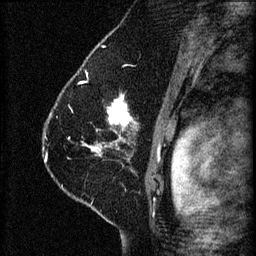
Breast MRI (dynamic contrast-enhanced), one sagittal slice. 3 images stored at this slice position (order not interpretable as contrast timing). 1.5 T. TE 4.2 ms, TR 8.2 ms. 2 mm slice thickness. 256 × 256 image matrix, field of view 180 × 180 mm. Patient: female, 41 years.
Structures marked on this image (semi-automatic segmentation, software-assisted and operator-edited):
- analysis volume of interest (the breast-tissue region the enhancement analysis was run in; not a lesion): bounding box (x1, y1, x2, y2) in pixels: (67, 92, 165, 173)
- tumour enhancement mask (voxels above the 70 % enhancement threshold inside the analysis volume of interest): (89, 96, 132, 153)